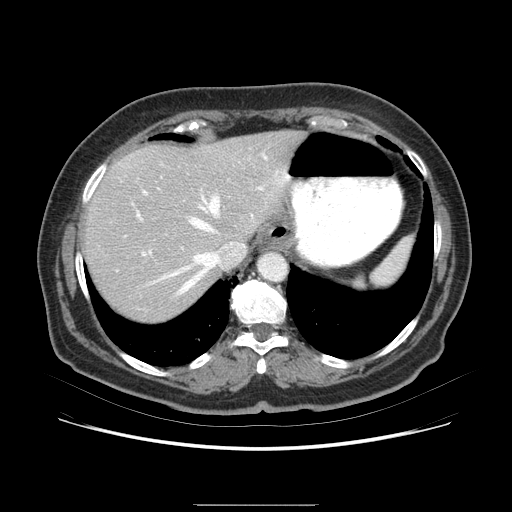
Contrast-enhanced abdominal CT (liver protocol), one axial slice; slice 63 of 79 in the series (ordered by position); soft-tissue window (W 400 / L 40 HU); 512 × 512 image matrix, field of view 380 × 380 mm. From the clinical record (not read from this slice): diagnosis: hepatocellular carcinoma (patient treated with transarterial chemoembolisation; whether this scan precedes or follows treatment is not stated here); TNM stage (as recorded): Stage-I; Child-Pugh class: A; tumour differentiation: poorly differentiated; tumour nodularity: uninodular.
Outlined on this slice (semi-automatically segmented with operator editing):
- liver parenchyma outside the tumour (the mass and vessels are separate outlines, so this box may not span the whole liver): bounding box (x1, y1, x2, y2) in pixels: (90, 136, 312, 302)
- liver vessels: (119, 153, 304, 268)